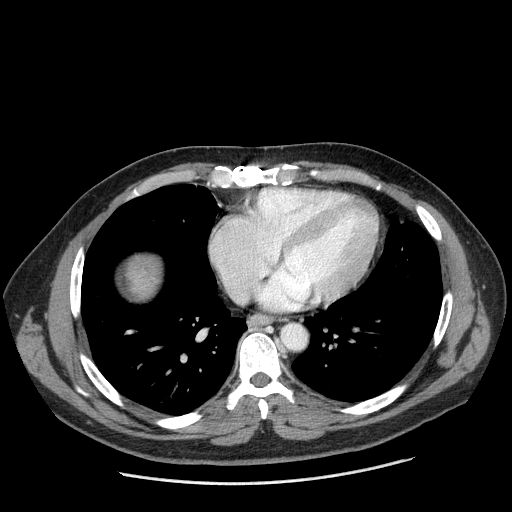
Contrast-enhanced abdominal CT (liver protocol), one axial slice; reconstruction kernel STANDARD; 120 kVp; one of 2 acquisitions stored at this slice position; soft-tissue window (W 400 / L 40 HU); 2.5 mm slice thickness; 512 × 512 image matrix. Case-level facts recorded for this patient, not image findings: diagnosis: hepatocellular carcinoma (patient treated with transarterial chemoembolisation; whether this scan precedes or follows treatment is not stated here); TNM stage (as recorded): Stage-II; Child-Pugh class: A; tumour differentiation: moderately differentiated.
Structures marked on this image (semi-automatic segmentation, software-assisted and operator-edited):
- liver parenchyma outside the tumour (the mass and vessels are separate outlines, so this box may not span the whole liver): bounding box (x1, y1, x2, y2) in pixels: (126, 256, 160, 297)